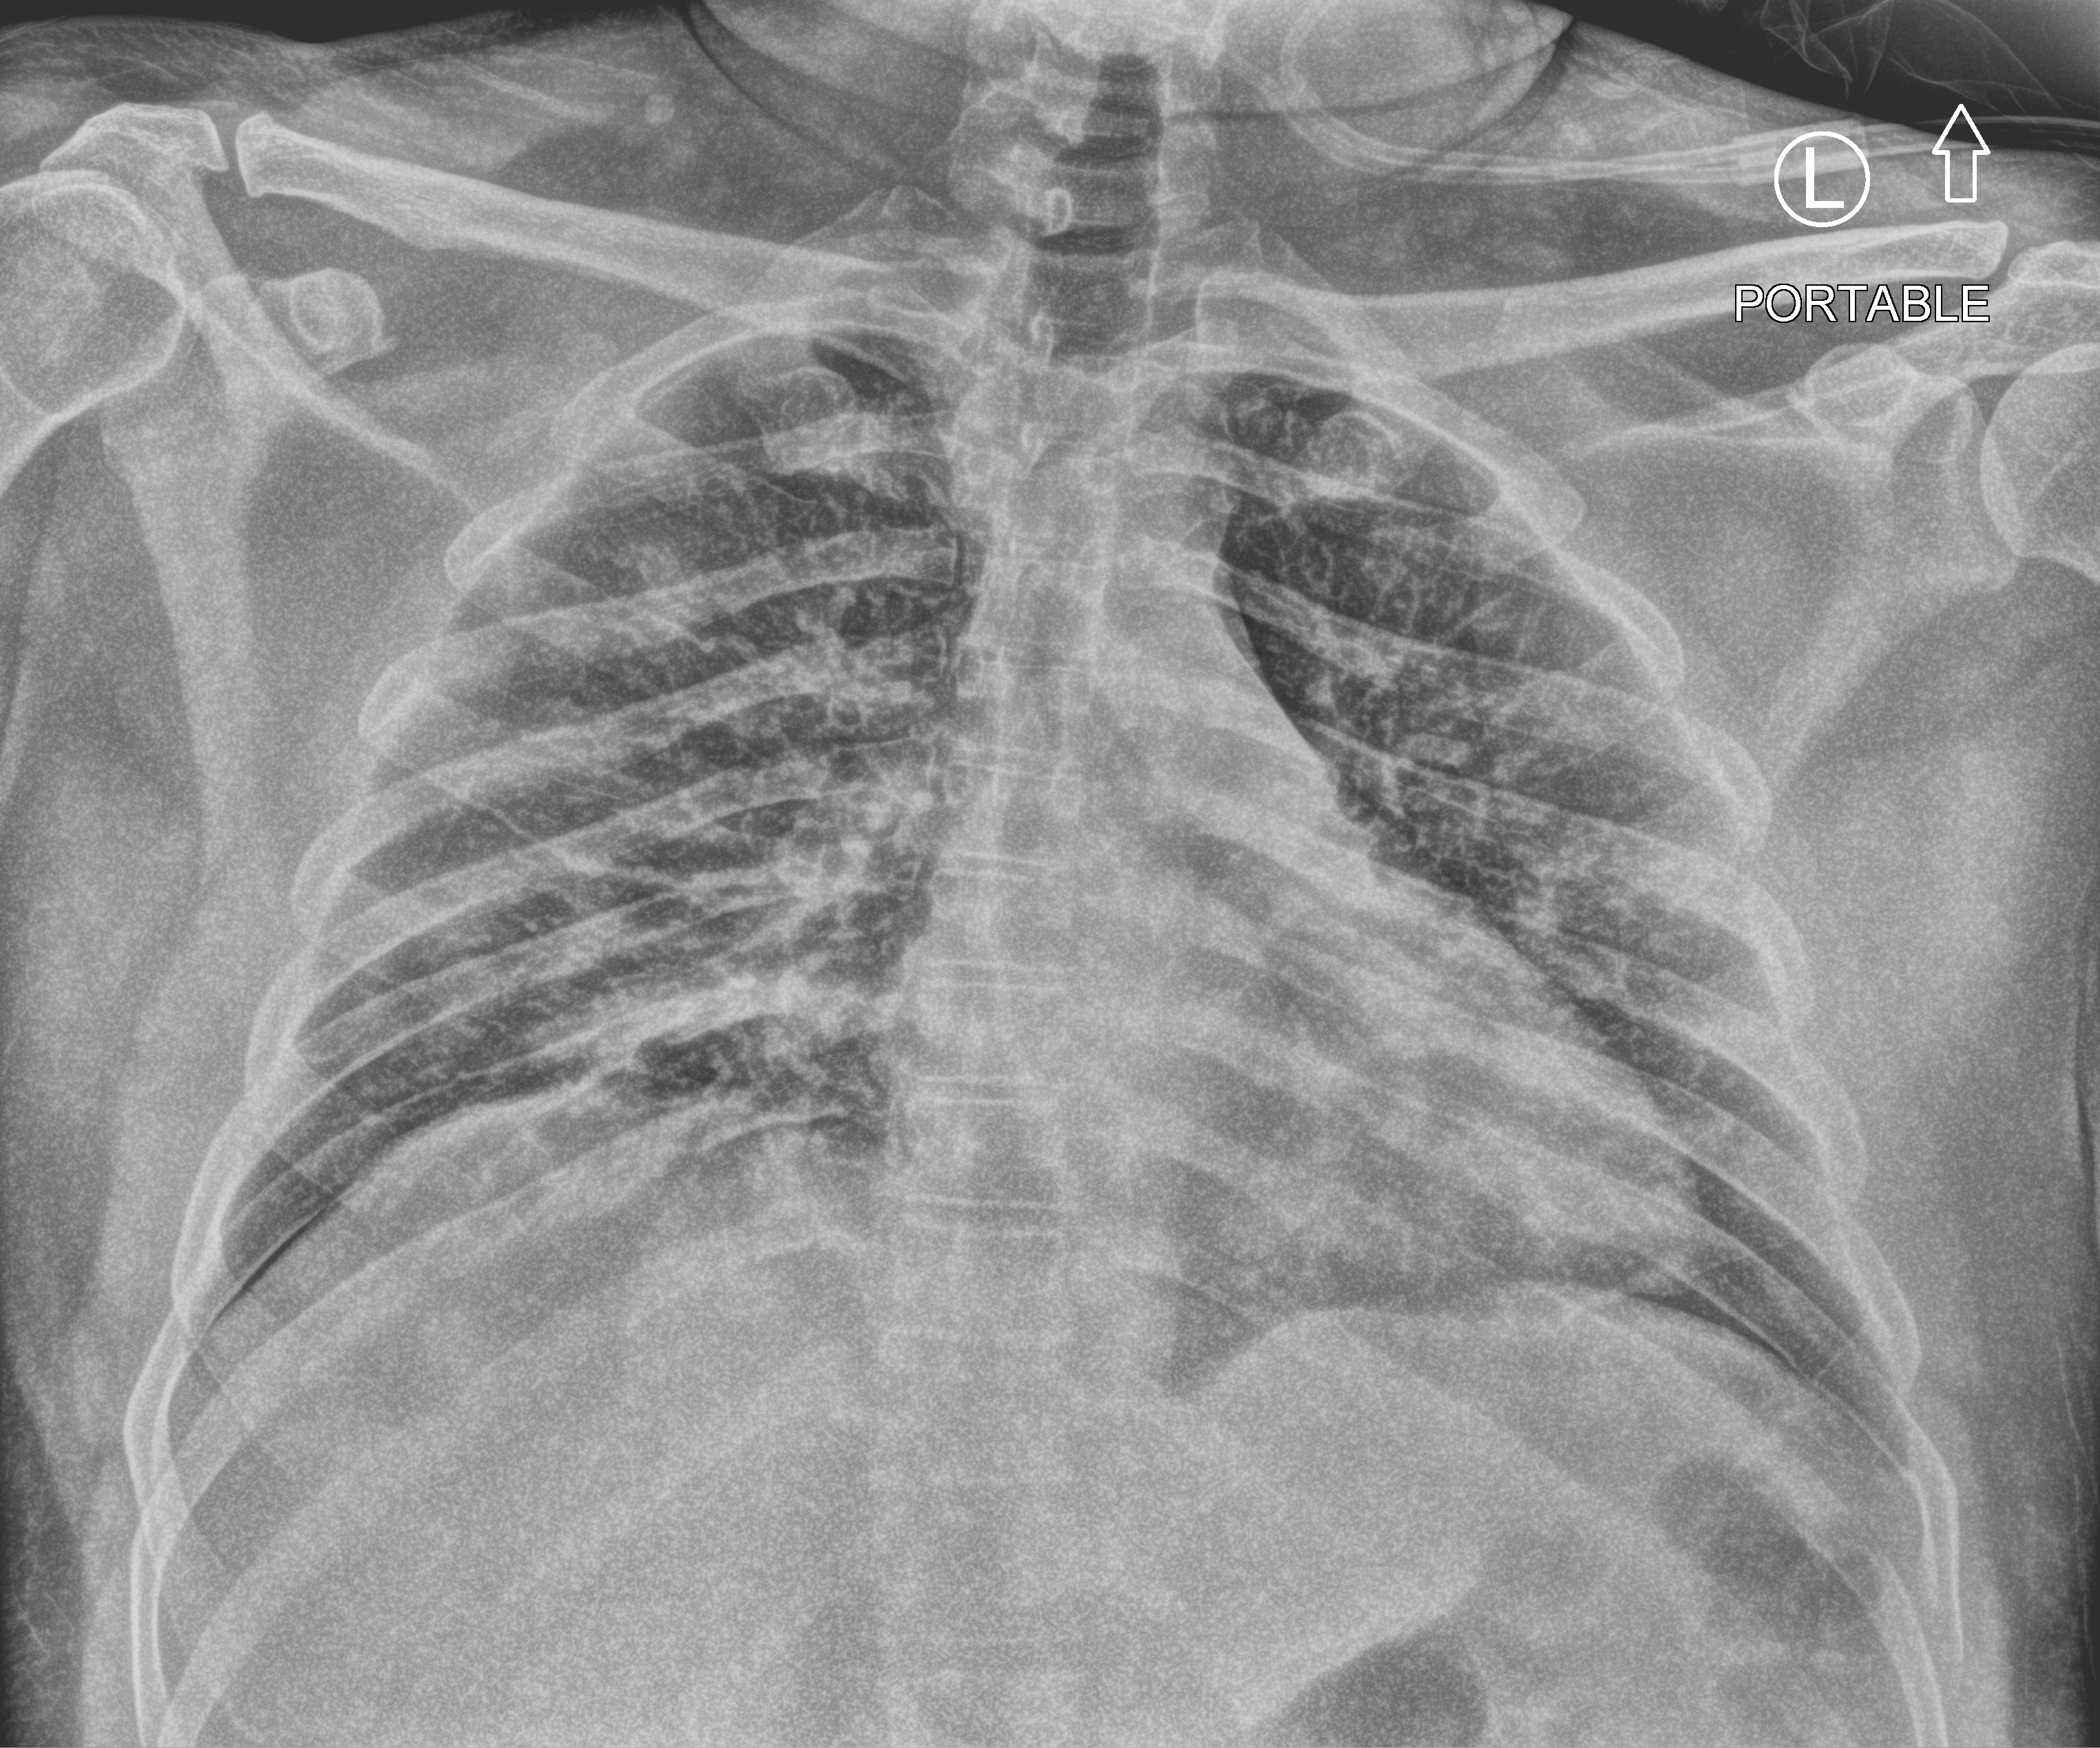
Chest X-ray (portable); anteroposterior (AP) projection. Adult patient hospitalised with COVID-19, age 18–59 years.
Admission-level facts for this patient (not findings on this image; timing relative to this image not recorded):
- smoking status (admission record): never